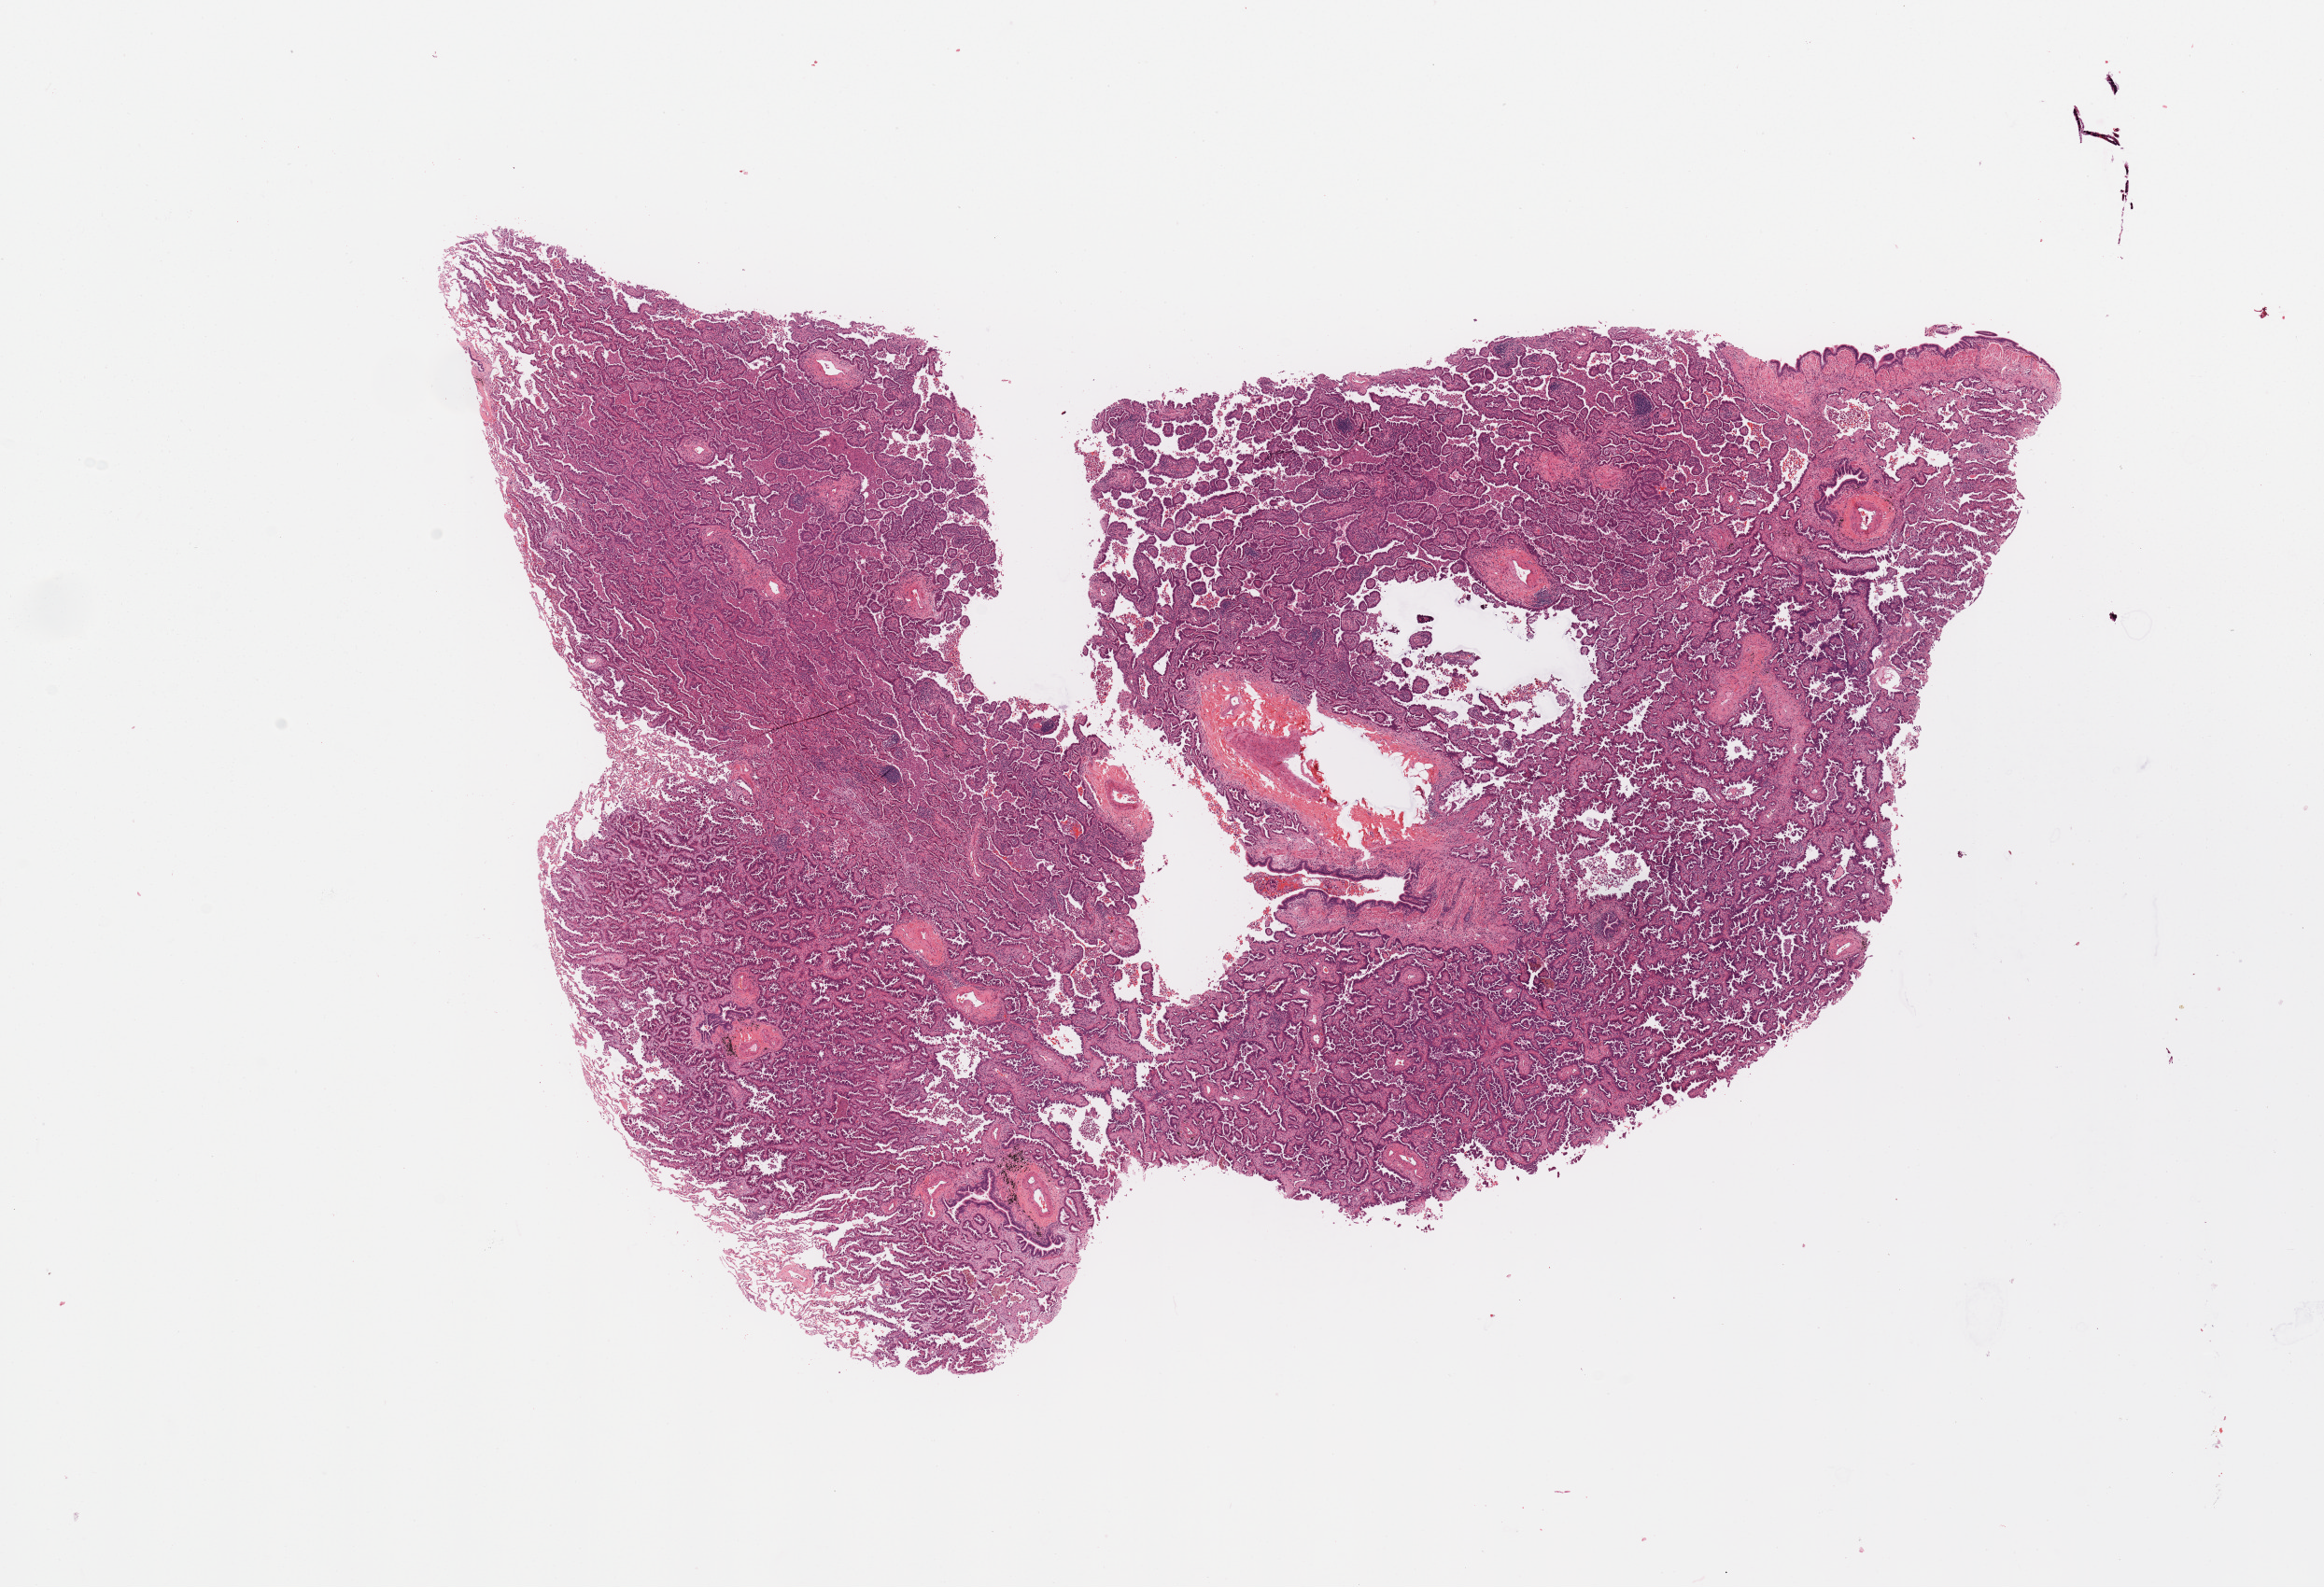
Hematoxylin and eosin (H&E) stained whole-slide image — whole scanned area (about 19.7 x 13.4 mm) shown as a low-resolution overview. Tumour tissue sample, sampled site: lung. Male, 56 y/o.
Diagnosis: Adenocarcinoma, NOS.